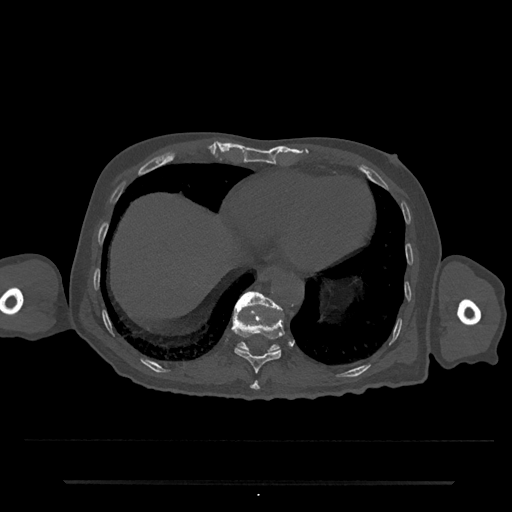
CT including the spine, one axial slice; slice 298 of 797 in the series (ordered by position); reconstruction kernel Br40s/3; bone window (W 1800 / L 400 HU); 0.5 mm slice thickness; 512 × 512 image matrix, field of view 427 × 427 mm. Patient: male, 74 years. Case-level facts recorded for this patient, not image findings: primary cancer: prostate.
Outlined on this slice (semi-automatically segmented with operator editing):
- T10 vertebra: bounding box [x1, y1, x2, y2] px = [232, 314, 285, 374]
- T11 vertebra: [234, 291, 283, 352]
- T9 vertebra: [250, 381, 260, 391]